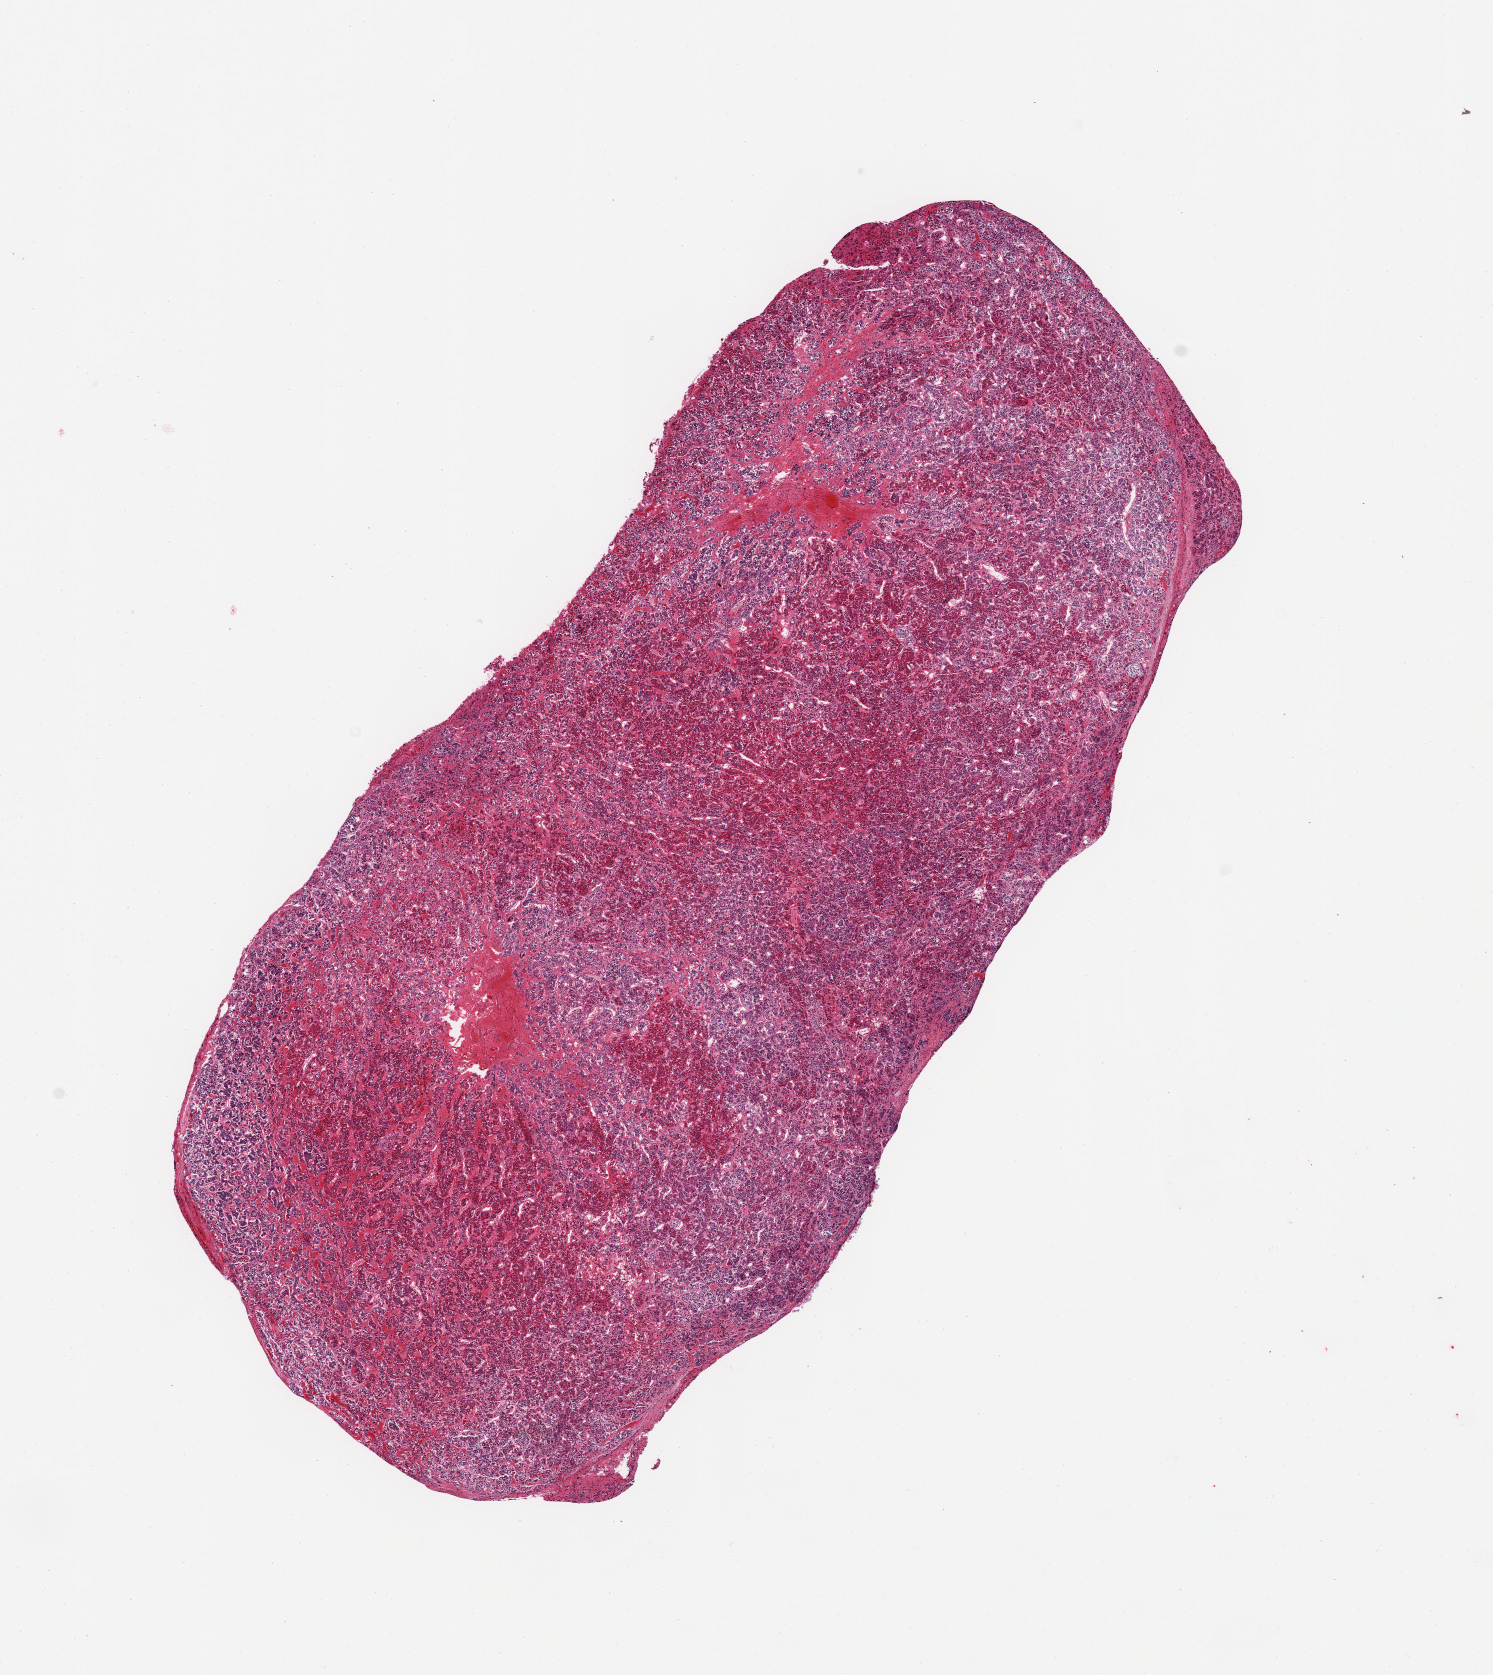
Digitized hematoxylin and eosin (H&E)-stained section — whole scanned area (about 11.8 x 13.3 mm) shown as a low-resolution overview; PAXgene-fixed paraffin-embedded (PFPE) section; section of pituitary (target tissue); tissue donor sample. Male donor.
Pathologist's review note for this sample: 1 piece; all adenohypophysis.